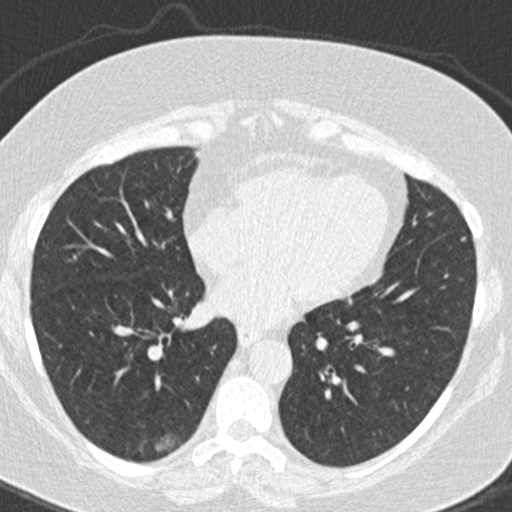
Axial slice from a low-dose chest CT screening exam, baseline screening round, lung window (W 1500 / L -600 HU), 2 mm slice thickness, 512 × 512 image matrix. Female, age 63 years at enrolment.
Lesion marked by an expert reader, bounding box <147,422,186,460> (left, top, right, bottom; pixels). Reader record for this screening exam (exam-level; its link to the box is not recorded): non-calcified nodule or mass ≥4 mm, right lower lobe, 16 × 10 mm, poorly defined margins, ground glass attenuation. Official screen result: positive, change unspecified: nodule(s) >= 4 mm or enlarging nodule(s), mass(es), or other non-specific abnormalities suspicious for lung cancer. Lung cancer was diagnosed 246 days after this screen: bronchiolo-alveolar adenocarcinoma, NOS, right lower lobe, well differentiated (G1), stage IA (AJCC 6th edition), 12 mm at pathology.